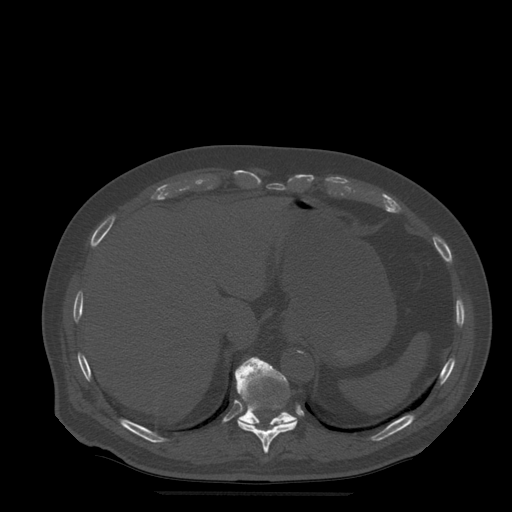
CT including the spine, one axial slice; position 259 of 522 along the scan axis; bone window (W 1800 / L 400 HU); 1.25 mm slice thickness; 512 × 512 image matrix, field of view 420 × 420 mm. Patient age 72 years. From the clinical record (not read from this slice): primary cancer: prostate.
Outlined on this slice (semi-automatically segmented with operator editing):
- T10 vertebra: bounding box <238,368,297,454> (left, top, right, bottom; pixels)
- T11 vertebra: <235,357,298,426>